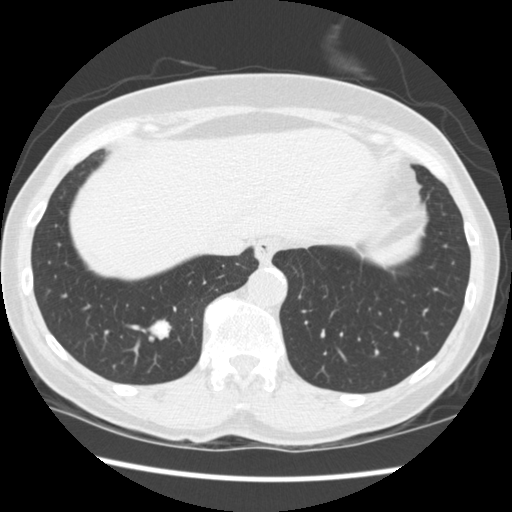
Low-dose screening chest CT, one axial slice; slice 60 of 262 in the series (ordered by position); 120 kVp; lung window (W 1500 / L -600 HU); 512 × 512 image matrix.
Outlined on this slice (outlined manually by an expert reader):
- lesion 1 (tumor, lower lobe of right lung): bounding box [x1, y1, x2, y2] px = [150, 320, 171, 339]